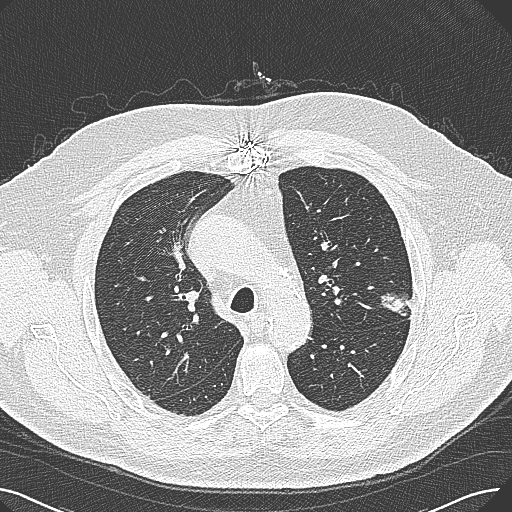
Low-dose screening chest CT, axial slice, first (baseline) screen, lung window (W 1500 / L -600 HU), 1 mm slice thickness, 120 kVp, slice 85 of 269 in the series. Male participant, aged 74 years at enrolment.
• Expert reader's lesion annotation, bounding box (x1, y1, x2, y2) in pixels: (370, 273, 425, 321).
• Reader record for this screening exam (exam-level; its link to the box is not recorded): non-calcified nodule or mass ≥4 mm, left upper lobe, 15 × 10 mm, poorly defined margins, soft tissue attenuation.
• Later outcome: lung cancer diagnosed 124 days after this screen — adenocarcinoma, NOS, left upper lobe, well differentiated (G1), stage IA (AJCC 6th edition), 26 mm at pathology.